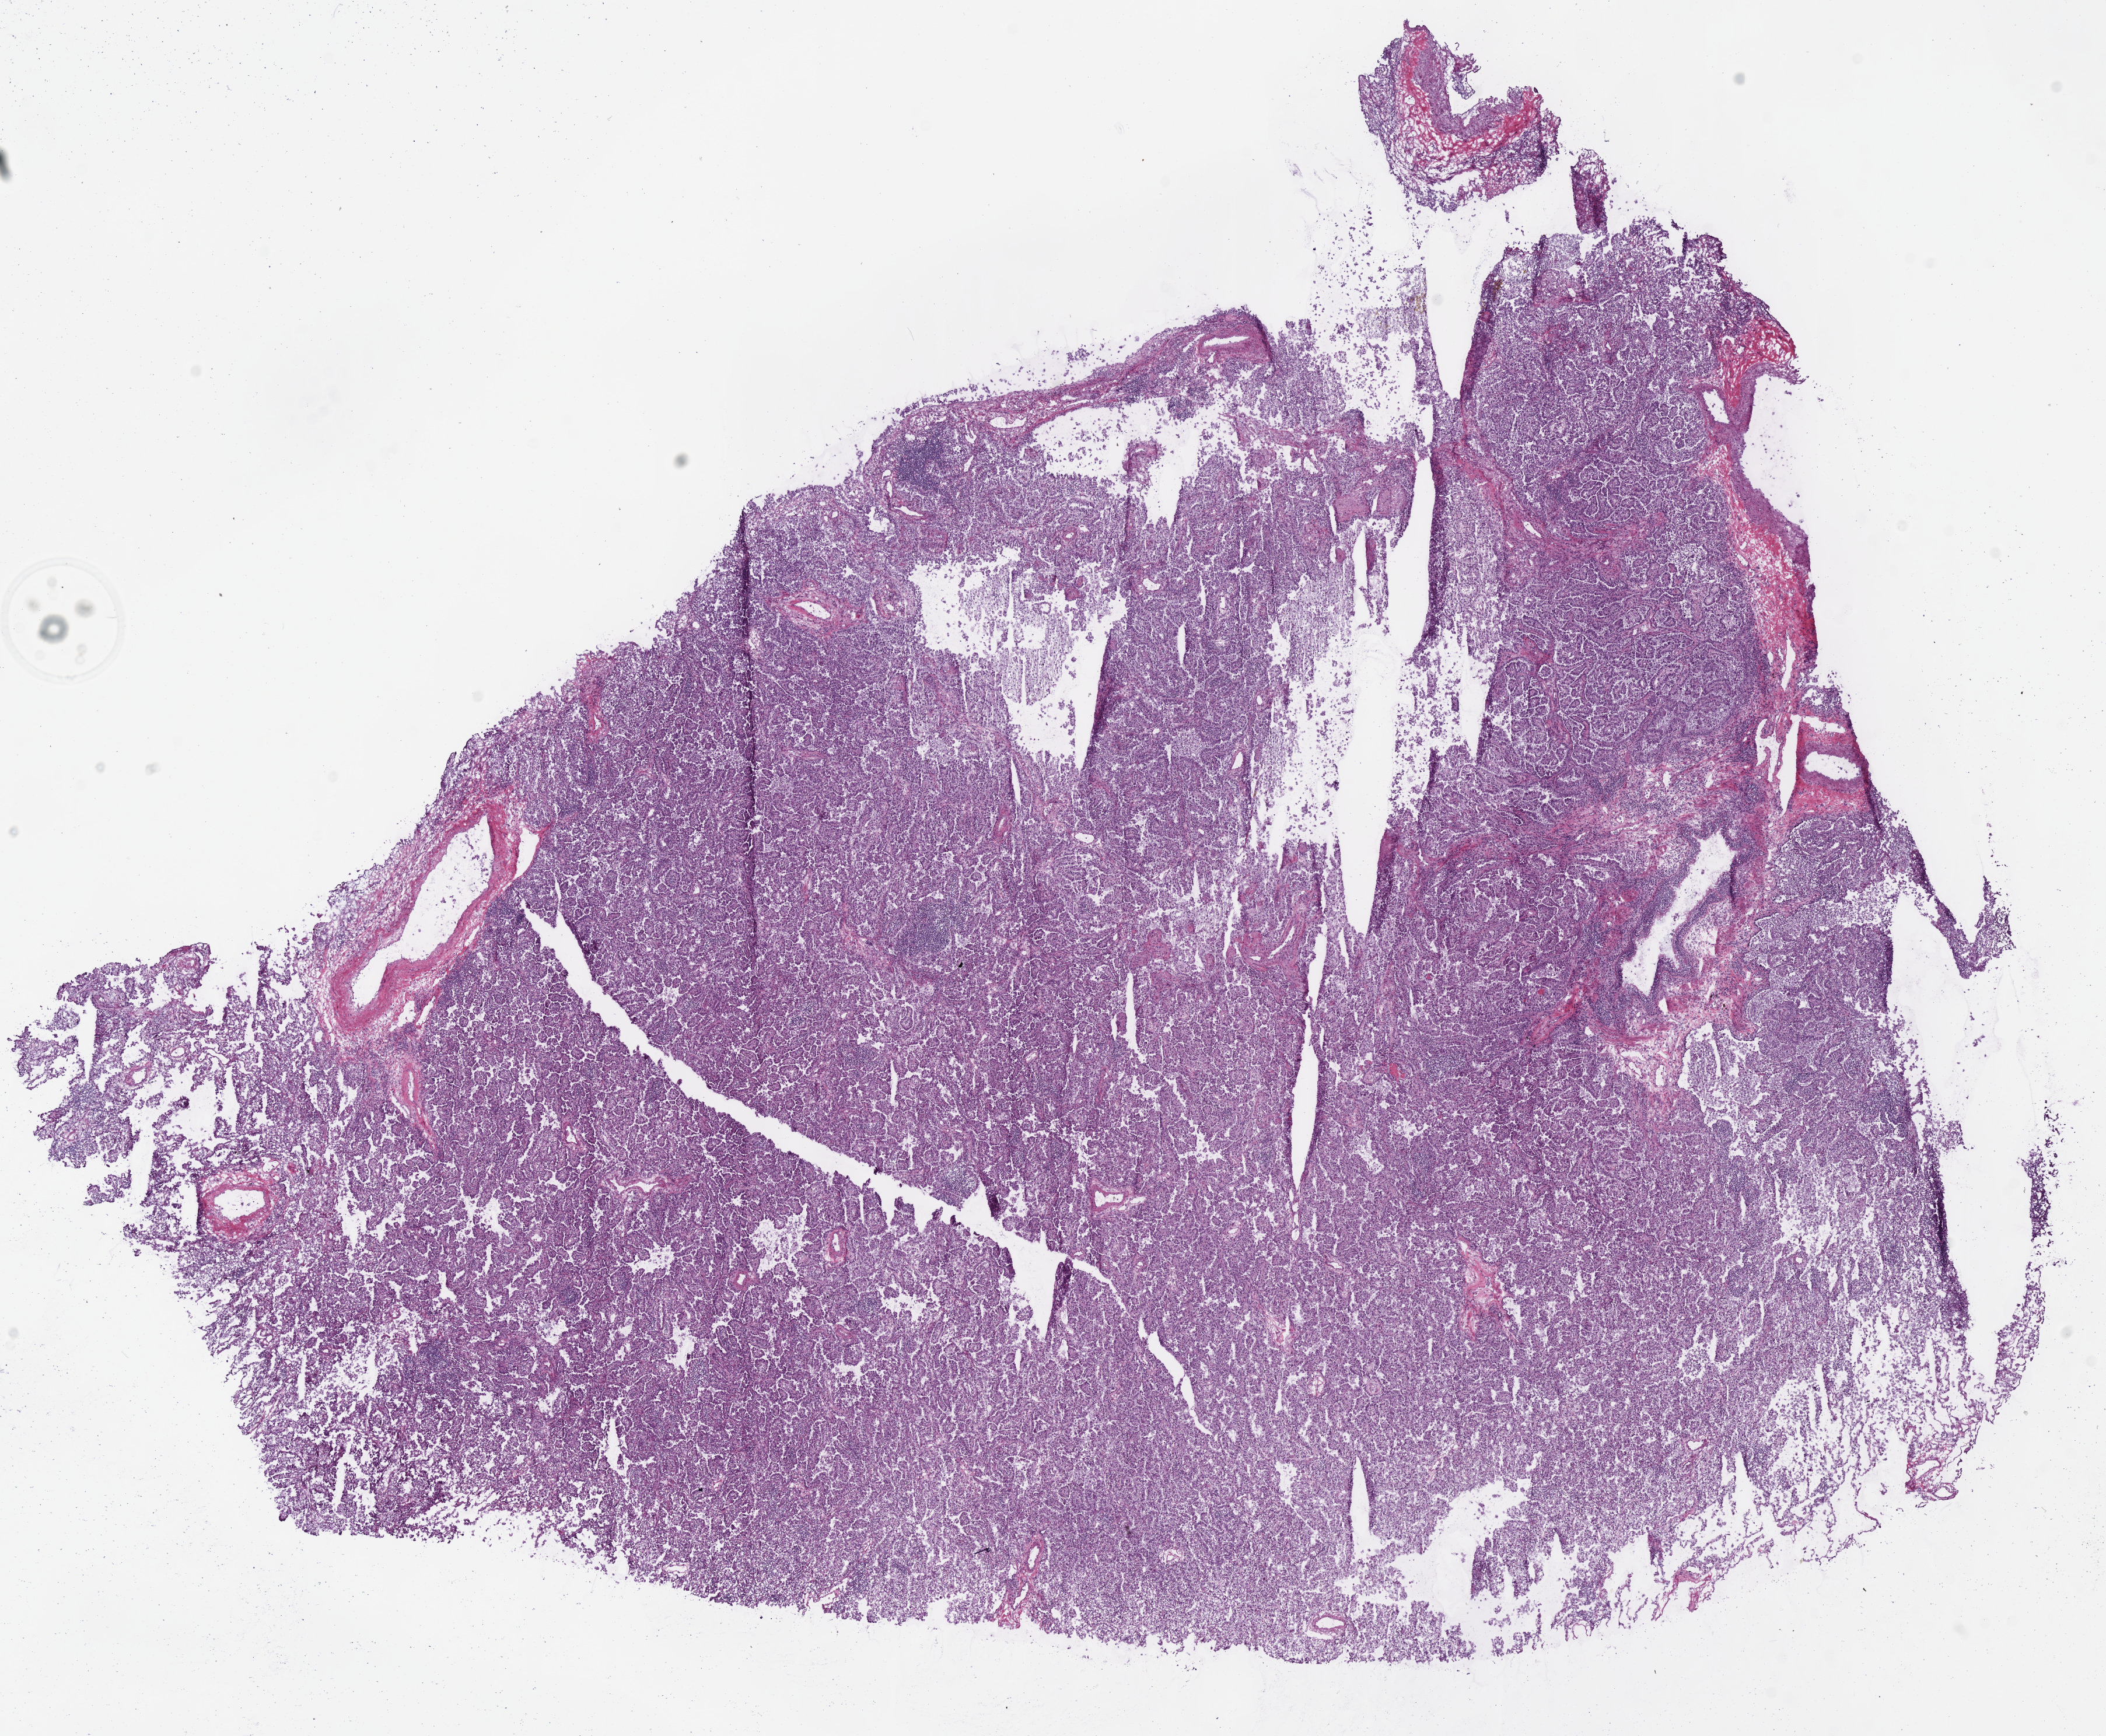
Whole-slide histology image, Hematoxylin and eosin (H&E) stained — whole scanned area (about 14.2 x 11.7 mm) shown as a low-resolution overview, frozen section from the bottom of the tissue portion, sample: primary tumour, lung. Female patient; age at initial diagnosis 63 years. Composition of this section per pathologist review: tumour cells 92%, tumour nuclei 90%, normal cells 2%, stromal cells 4%, necrosis 2%. Infiltration values recorded for this section: lymphocyte infiltration 3%.
- diagnosis: Adenocarcinoma with mixed subtypes (upper lobe, lung)
- AJCC pathologic stage: IIIA
- laterality: right